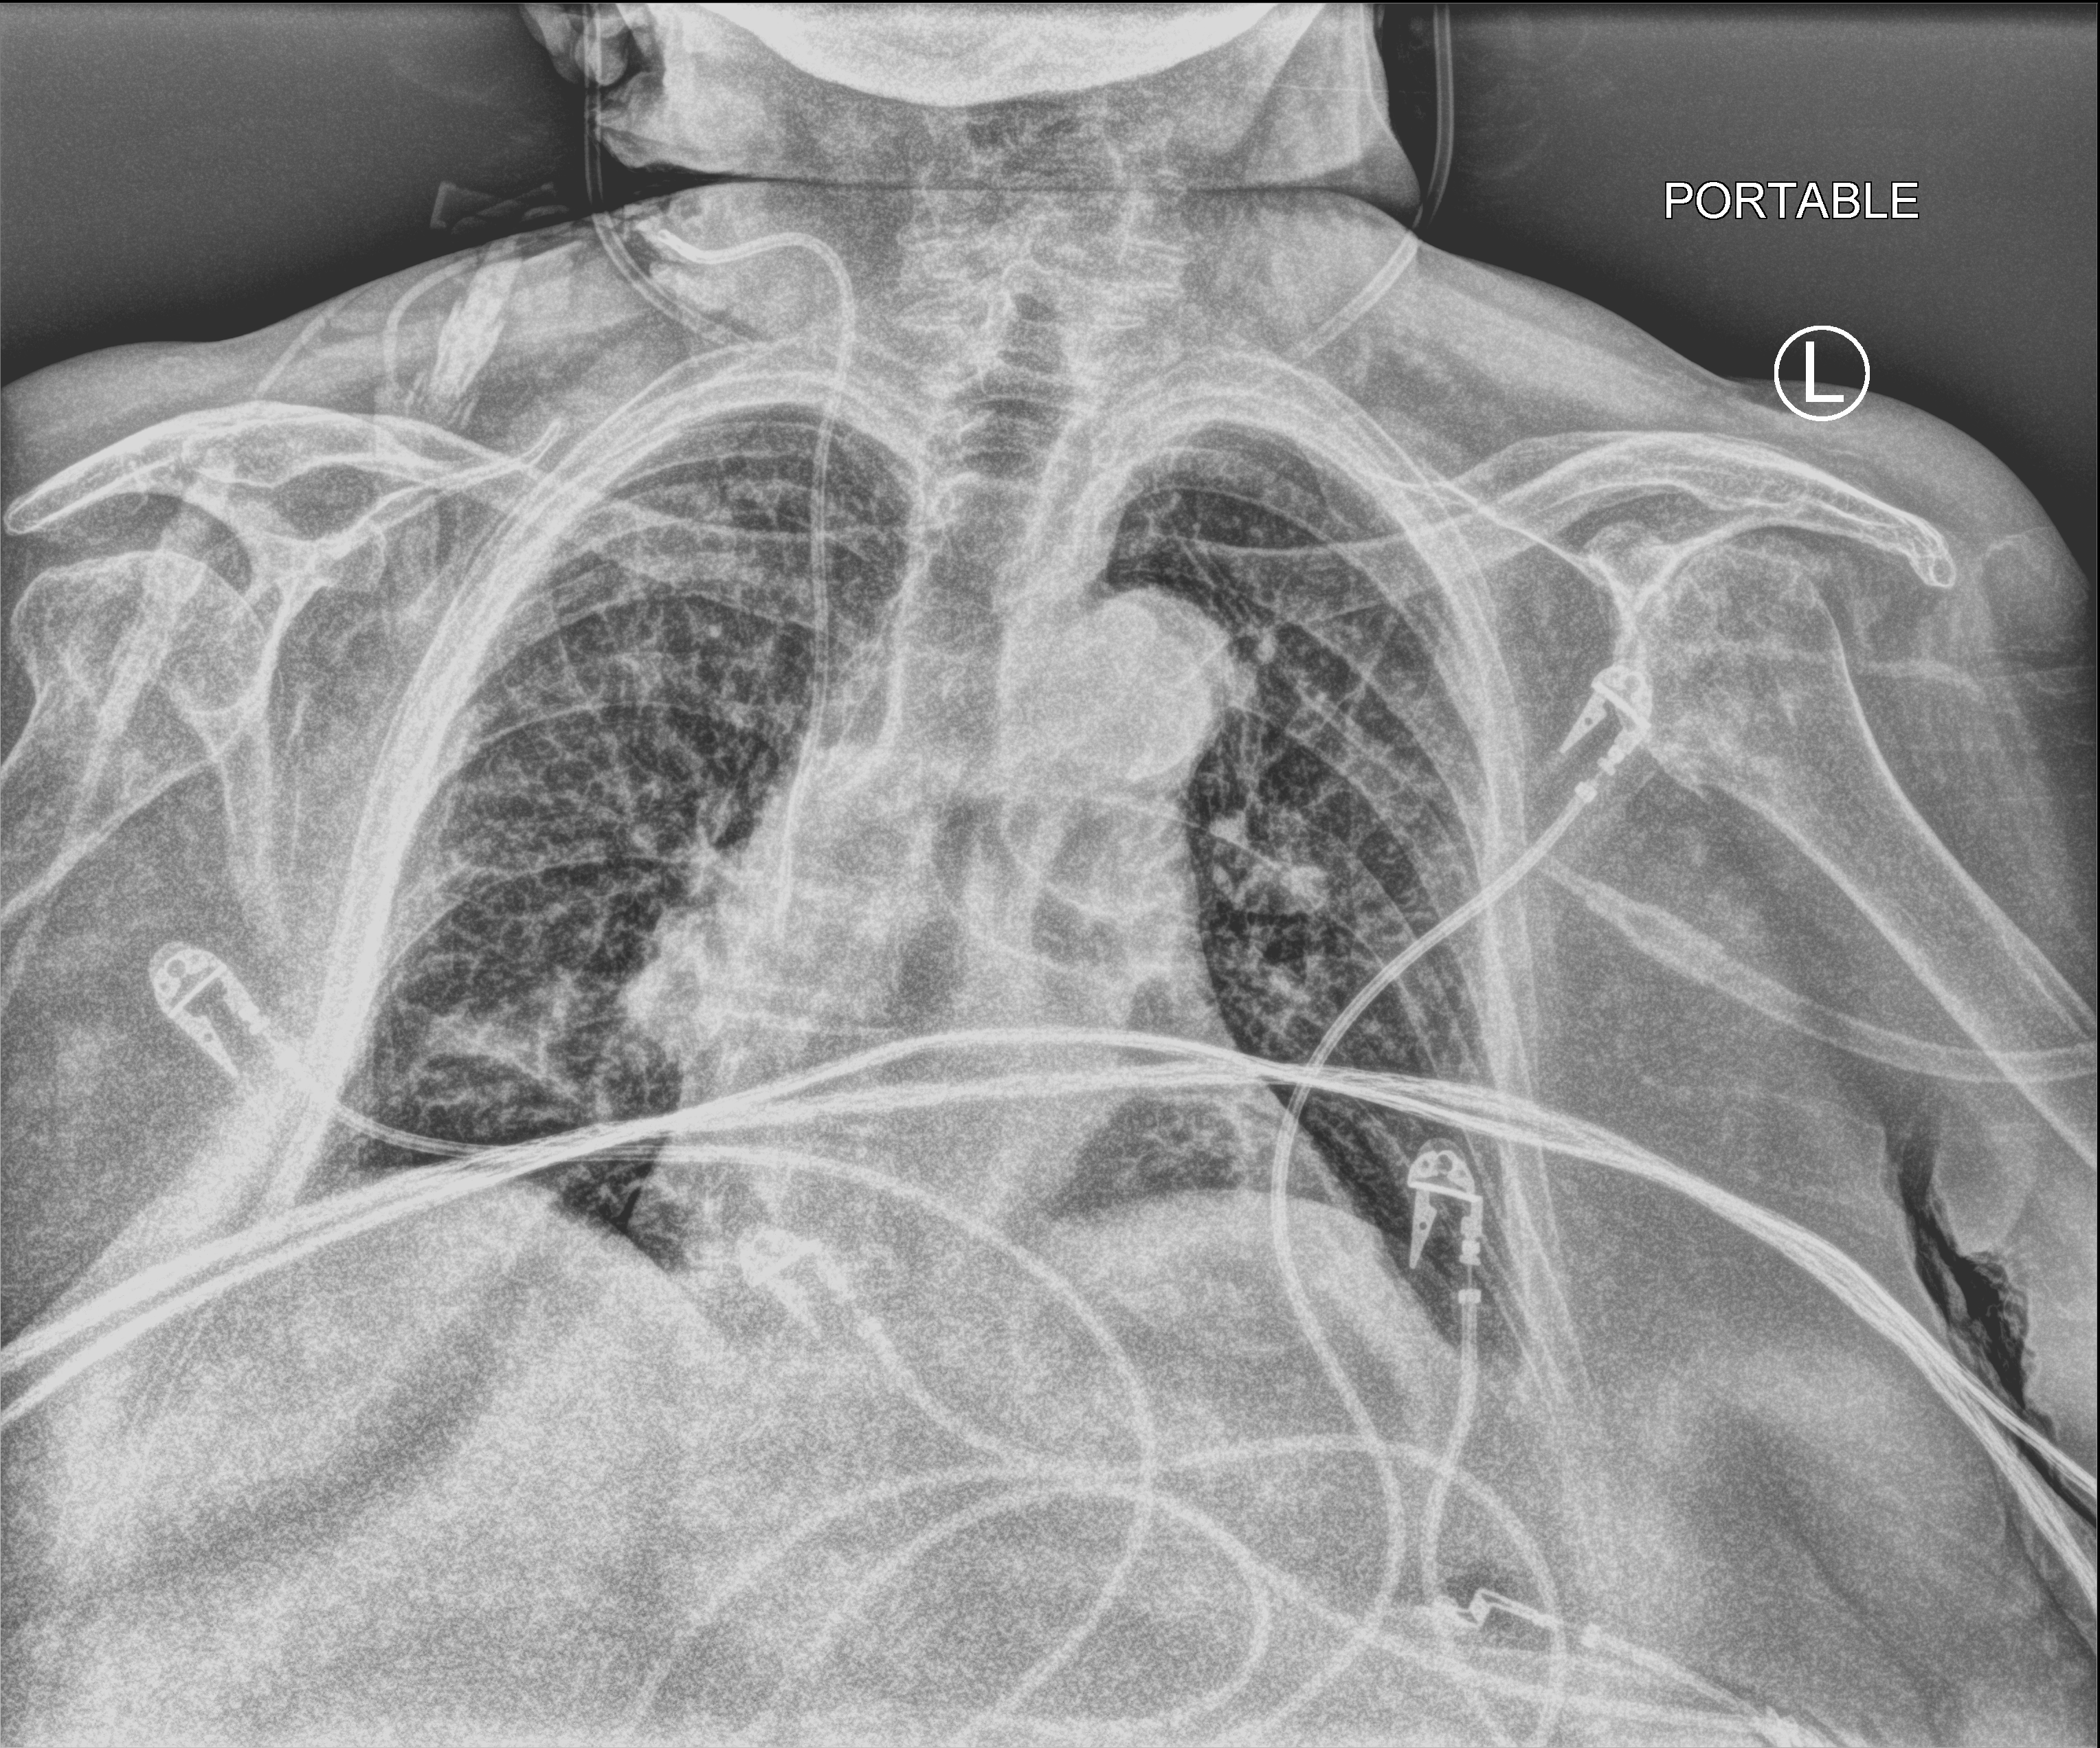
Portable chest radiograph, anteroposterior (AP) projection. Patient hospitalised with COVID-19; female, aged 75–90 years.
Hospital-stay facts (about this admission, not read from this image; timing relative to this image not recorded):
- mechanically ventilated during this hospital stay: no